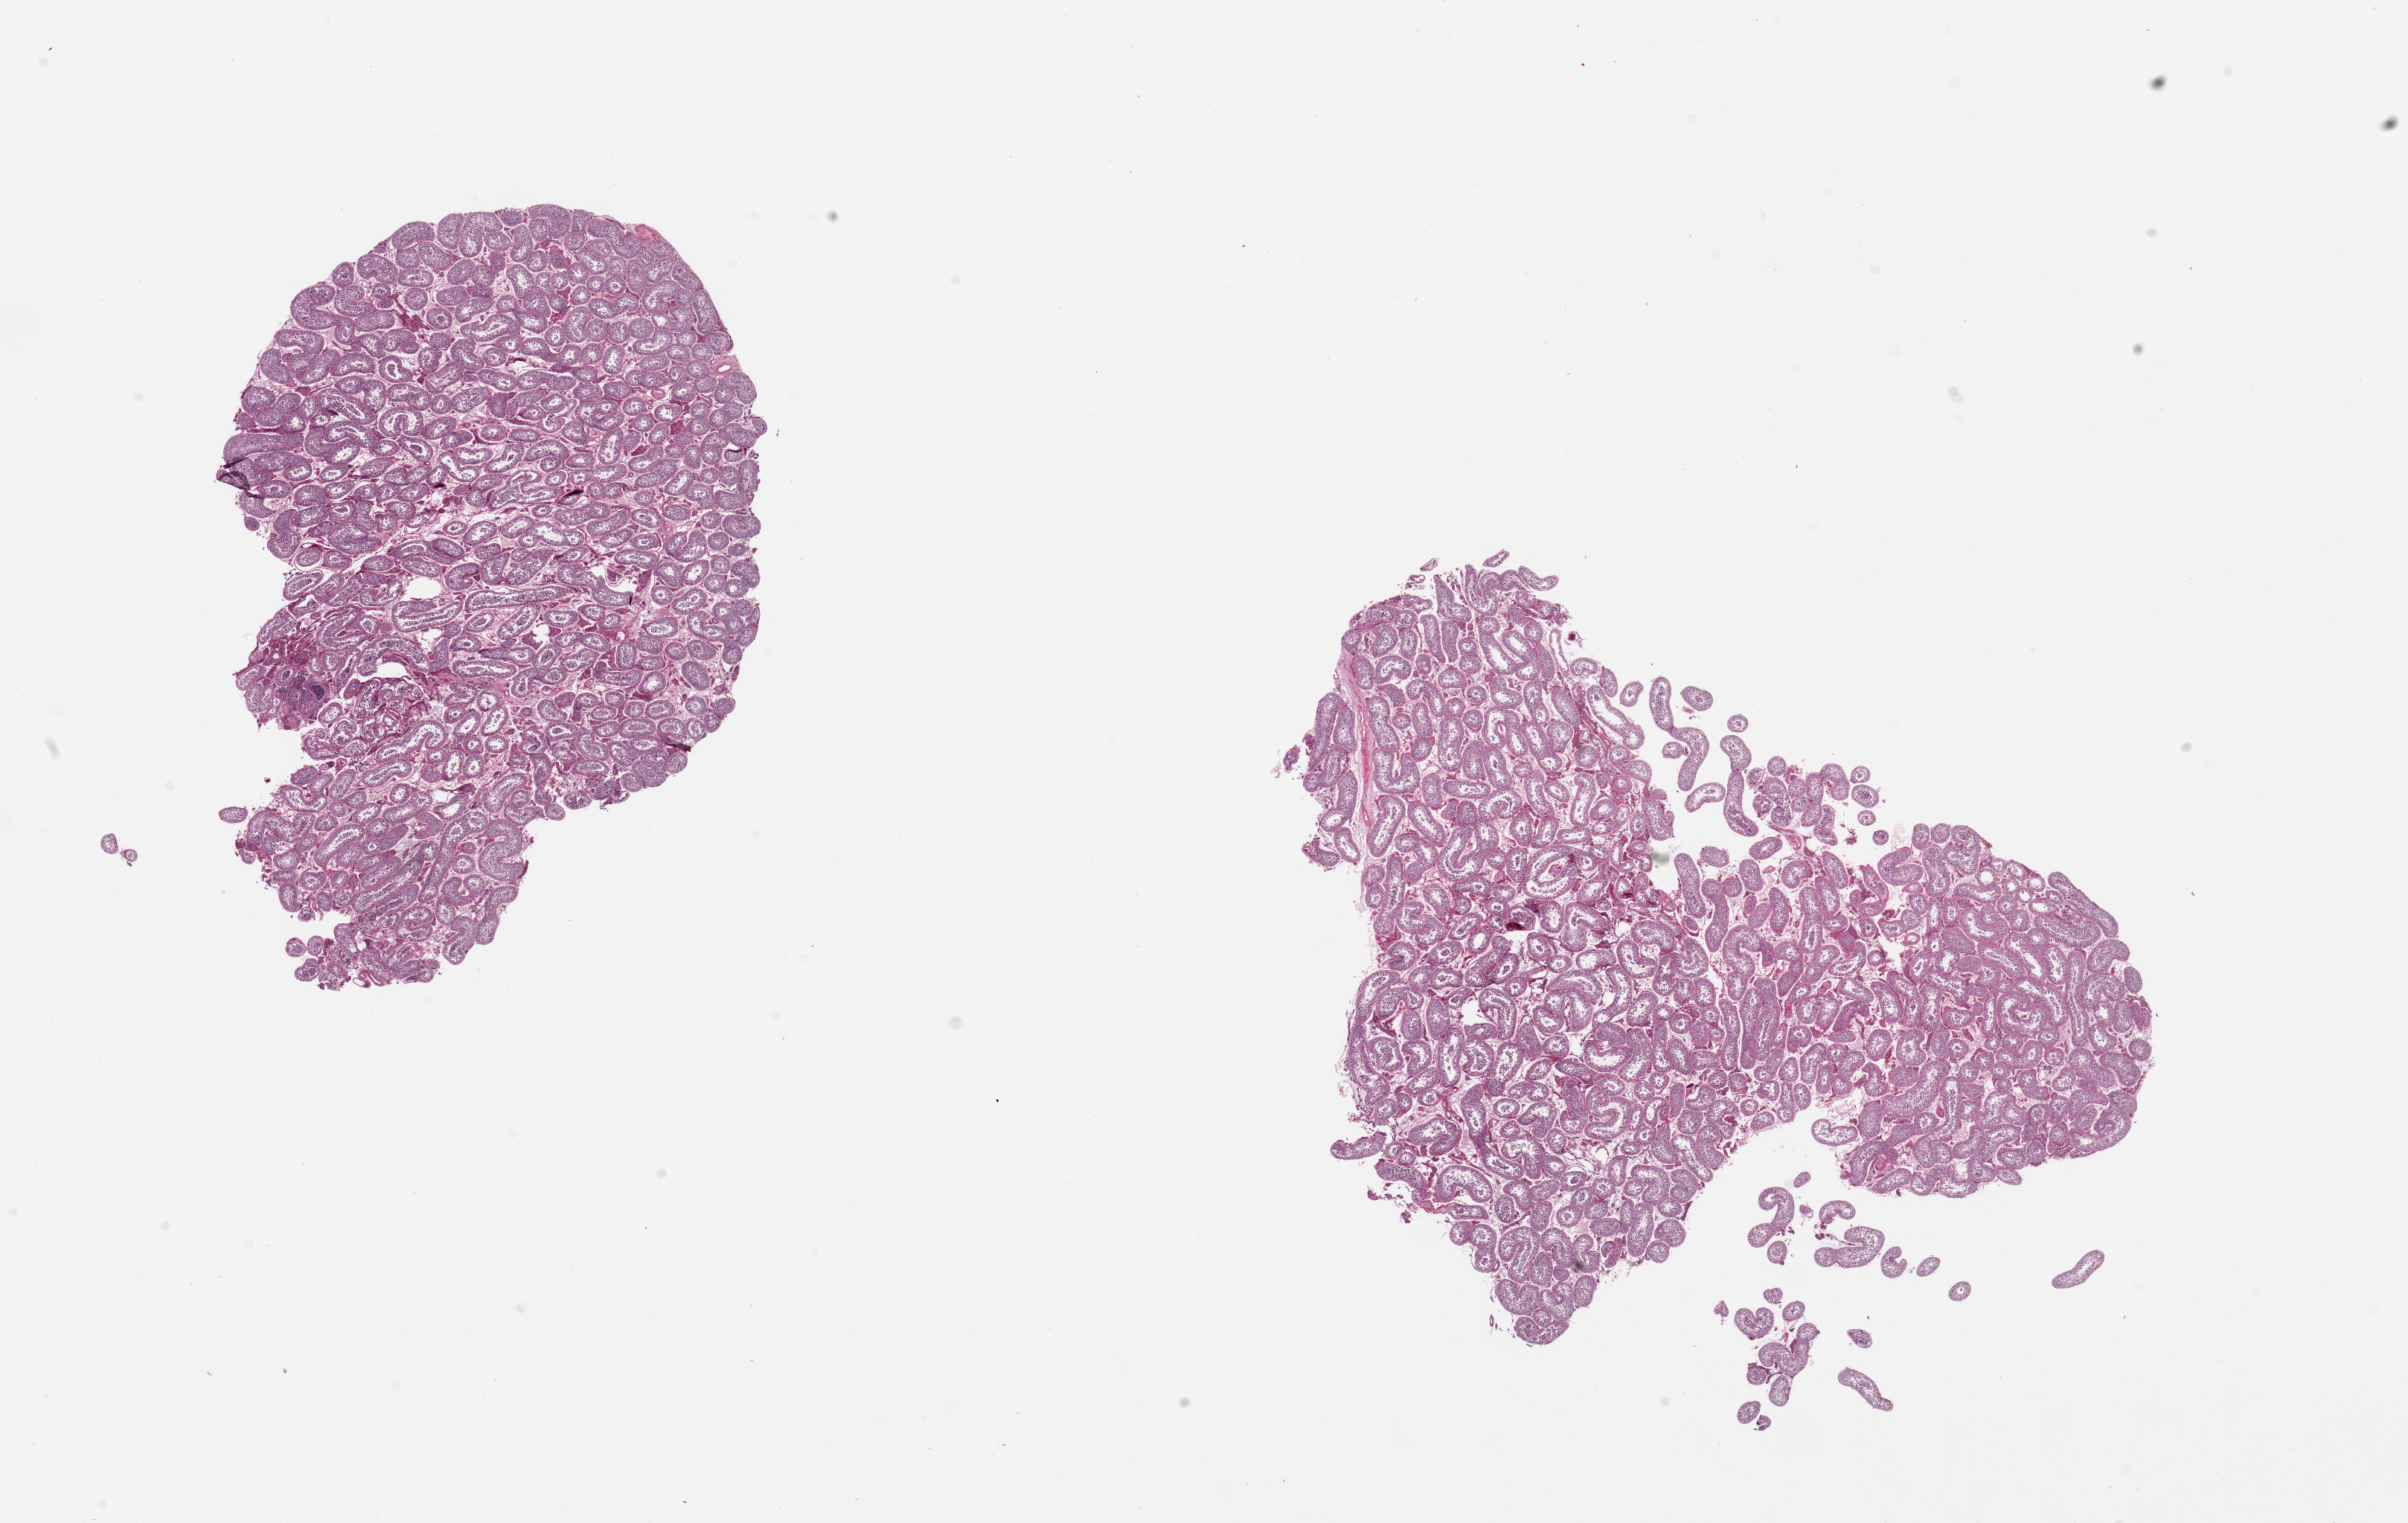
Digitized hematoxylin and eosin (H&E)-stained section, brightfield — low-resolution overview of the scanned area, about 25.6 x 16.2 mm, PAXgene-fixed paraffin-embedded (PFPE) section, section of testis (target tissue), donor tissue sample.
- review note (as recorded): 2 pieces, 10x7 and 9x6mm; spermatogenesis is present